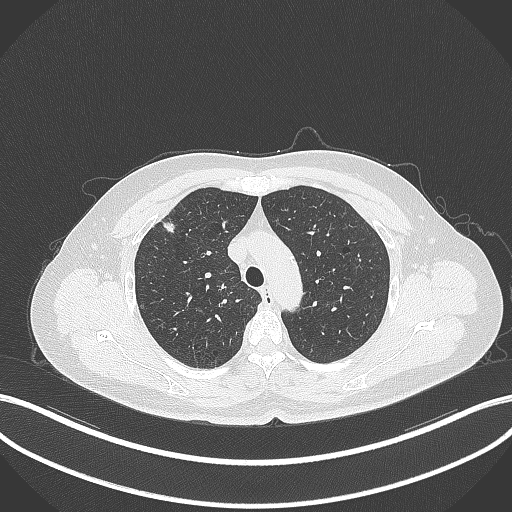
Chest CT, one axial slice. Position 276 of 353 along the scan axis. Reconstruction kernel B70f. Lung window (W 1500 / L -600 HU). 512 × 512 image matrix. Patient: female, 56 years. Case-level facts recorded for this patient, not image findings: clinical TNM (as recorded): T1c N0 M0.
Structures marked on this image (rectangle marked by the reading radiologist):
- lung tumour (recorded histology: adenocarcinoma): bounding box <162,218,184,243> (left, top, right, bottom; pixels)